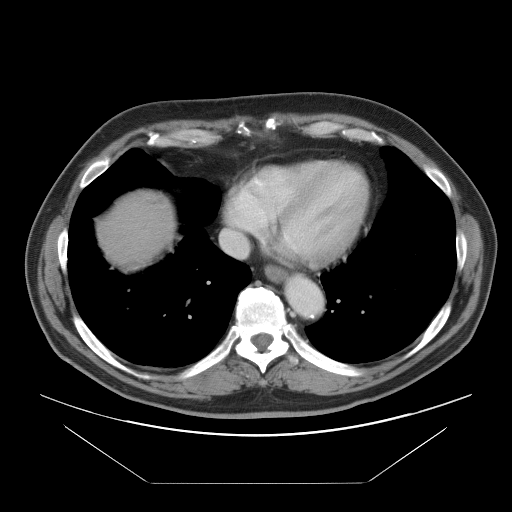
Contrast-enhanced abdominal CT, one axial slice. Slice 89 of 97 in the series (ordered by position). Intravenous contrast given. Soft-tissue window (W 400 / L 40 HU). 5 mm slice thickness. 512 × 512 image matrix. Male patient, age 62 years. From the clinical record (not read from this slice): diagnosis: colorectal cancer liver metastases, imaged before liver resection; multiple liver metastases: no; largest metastasis: 7 cm; disease in both lobes: yes.
Annotated regions visible in this slice (manually delineated by an expert):
- hepatic veins: box from (x=220, y=187) to (x=247, y=259) px
- liver: (x=103, y=198)–(x=173, y=261)
- planned liver remnant (the part of the liver to remain after resection): (x=103, y=199)–(x=174, y=261)